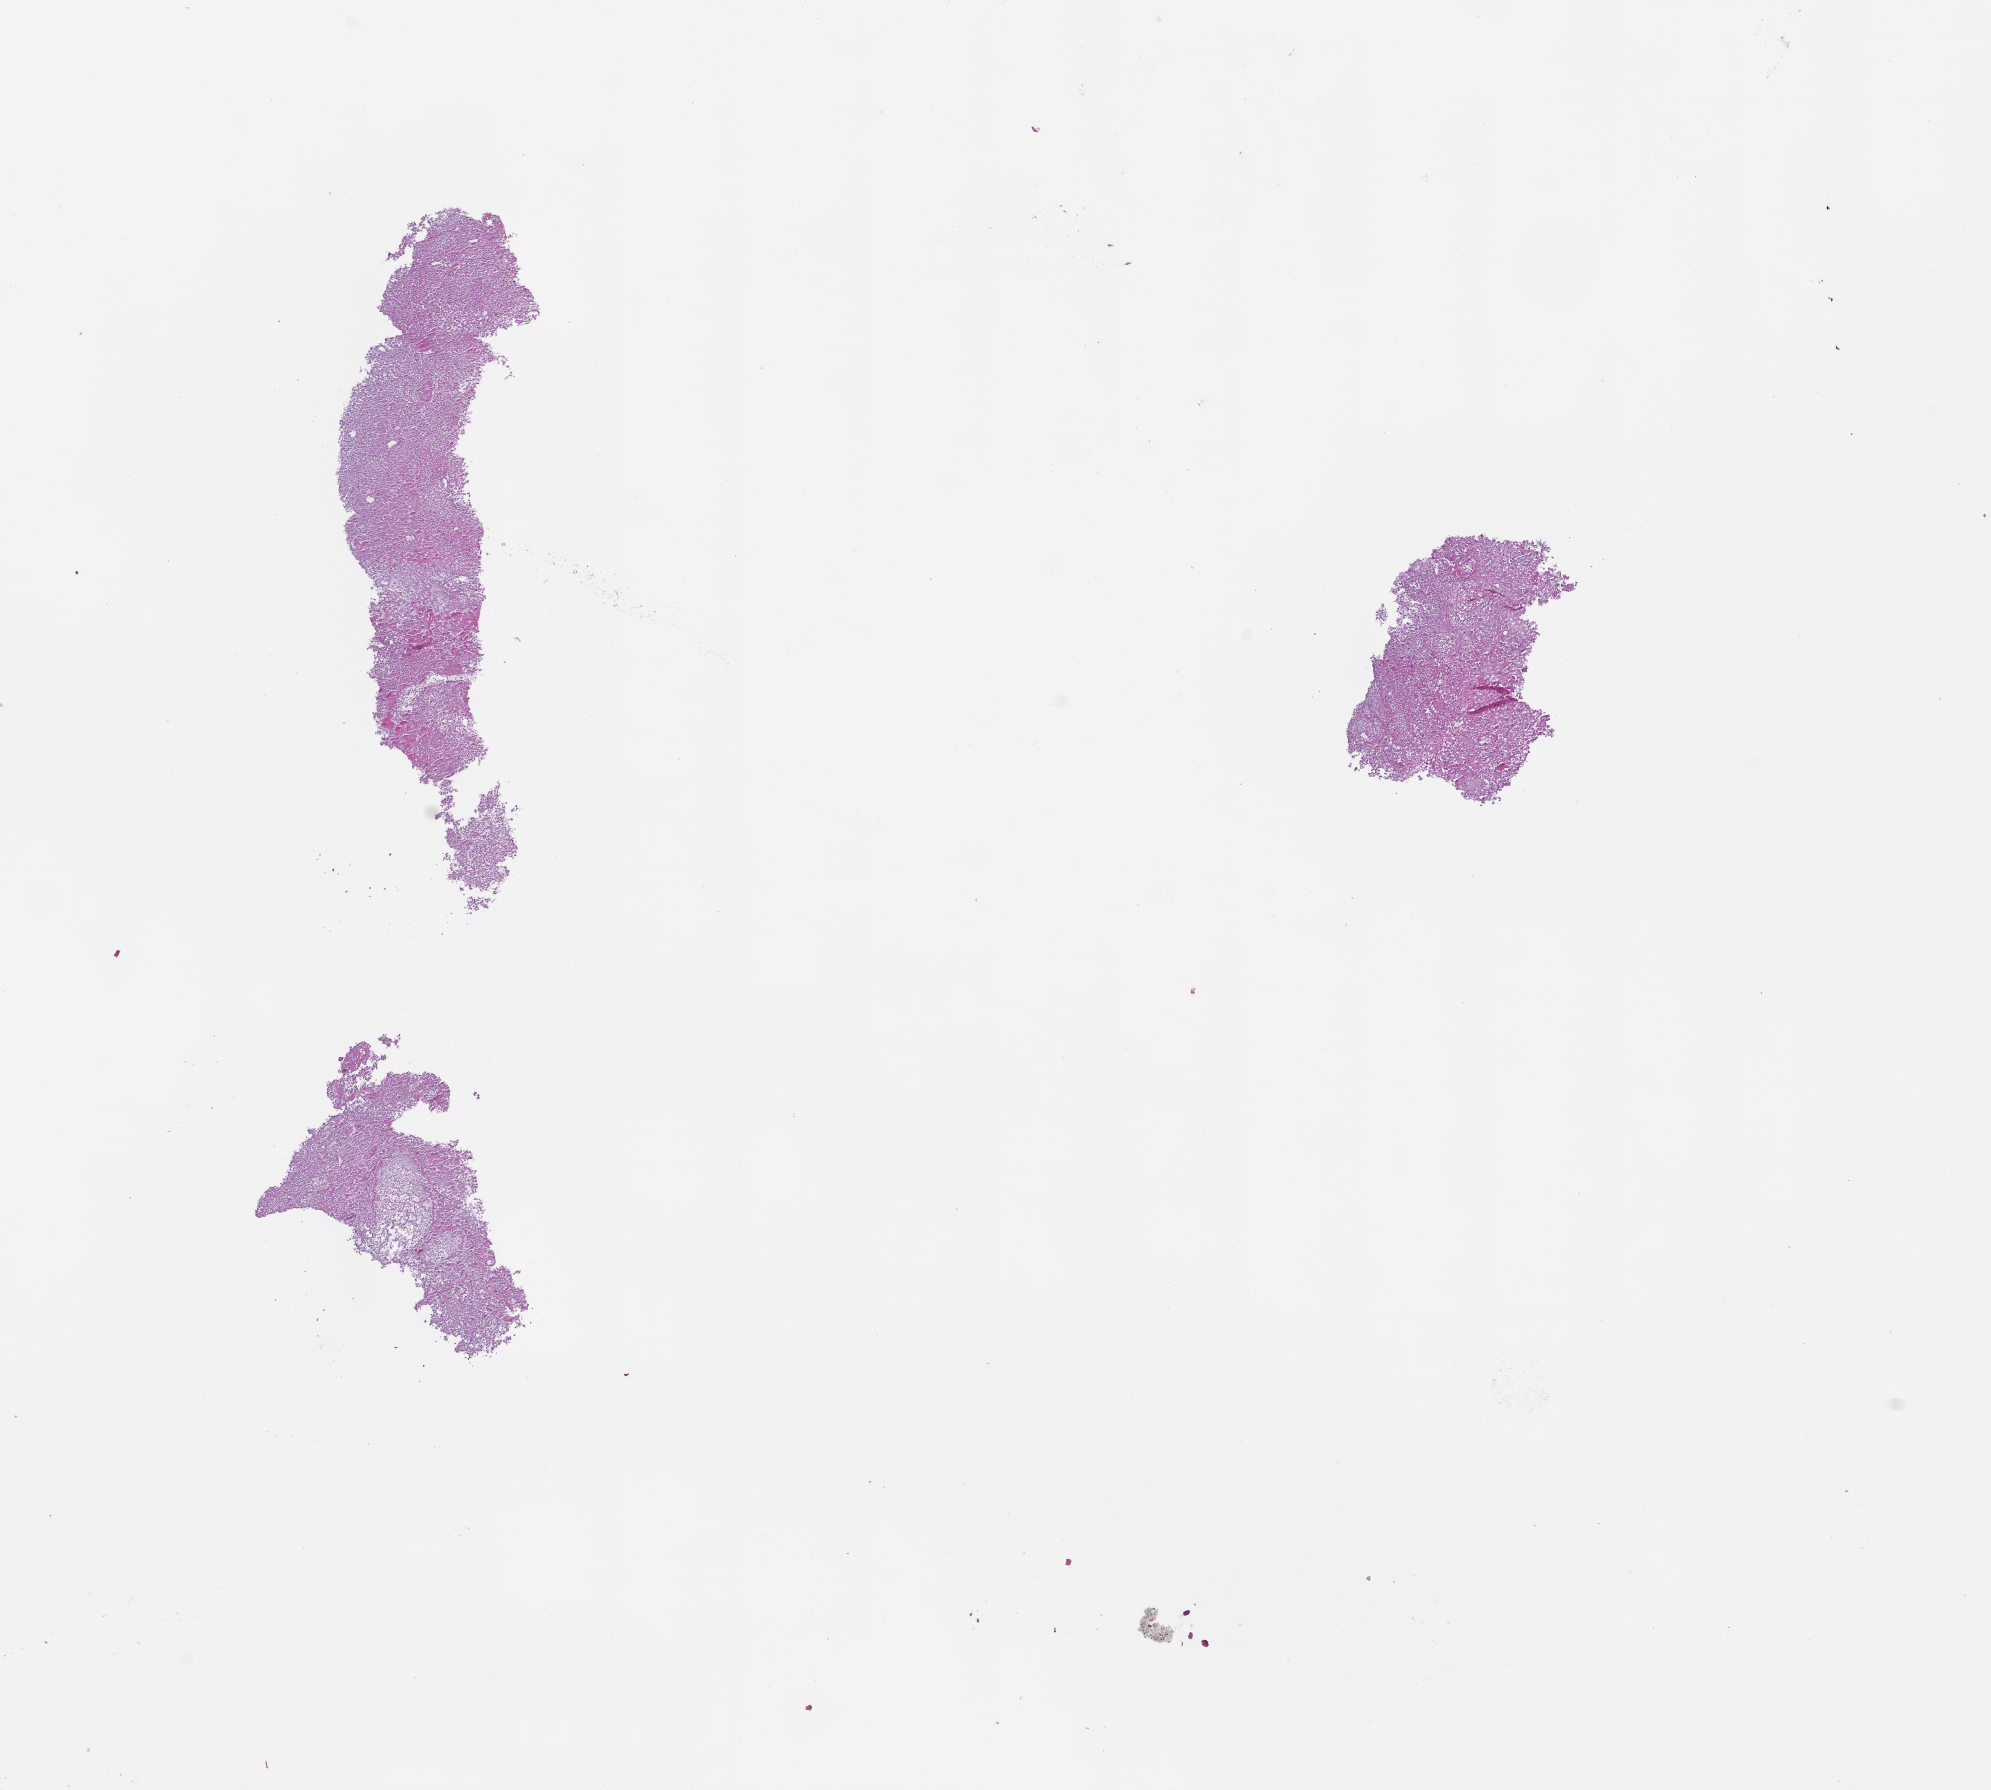
Hematoxylin and eosin (H&E) whole-slide image, a low-resolution overview of the entire scanned area, about 8.0 x 7.2 mm, formalin-fixed paraffin-embedded section, collected at baseline (before treatment). Patient sex: female.
This section: metastatic tumor tissue. Patient diagnosis (primary): Colorectal Carcinoma.